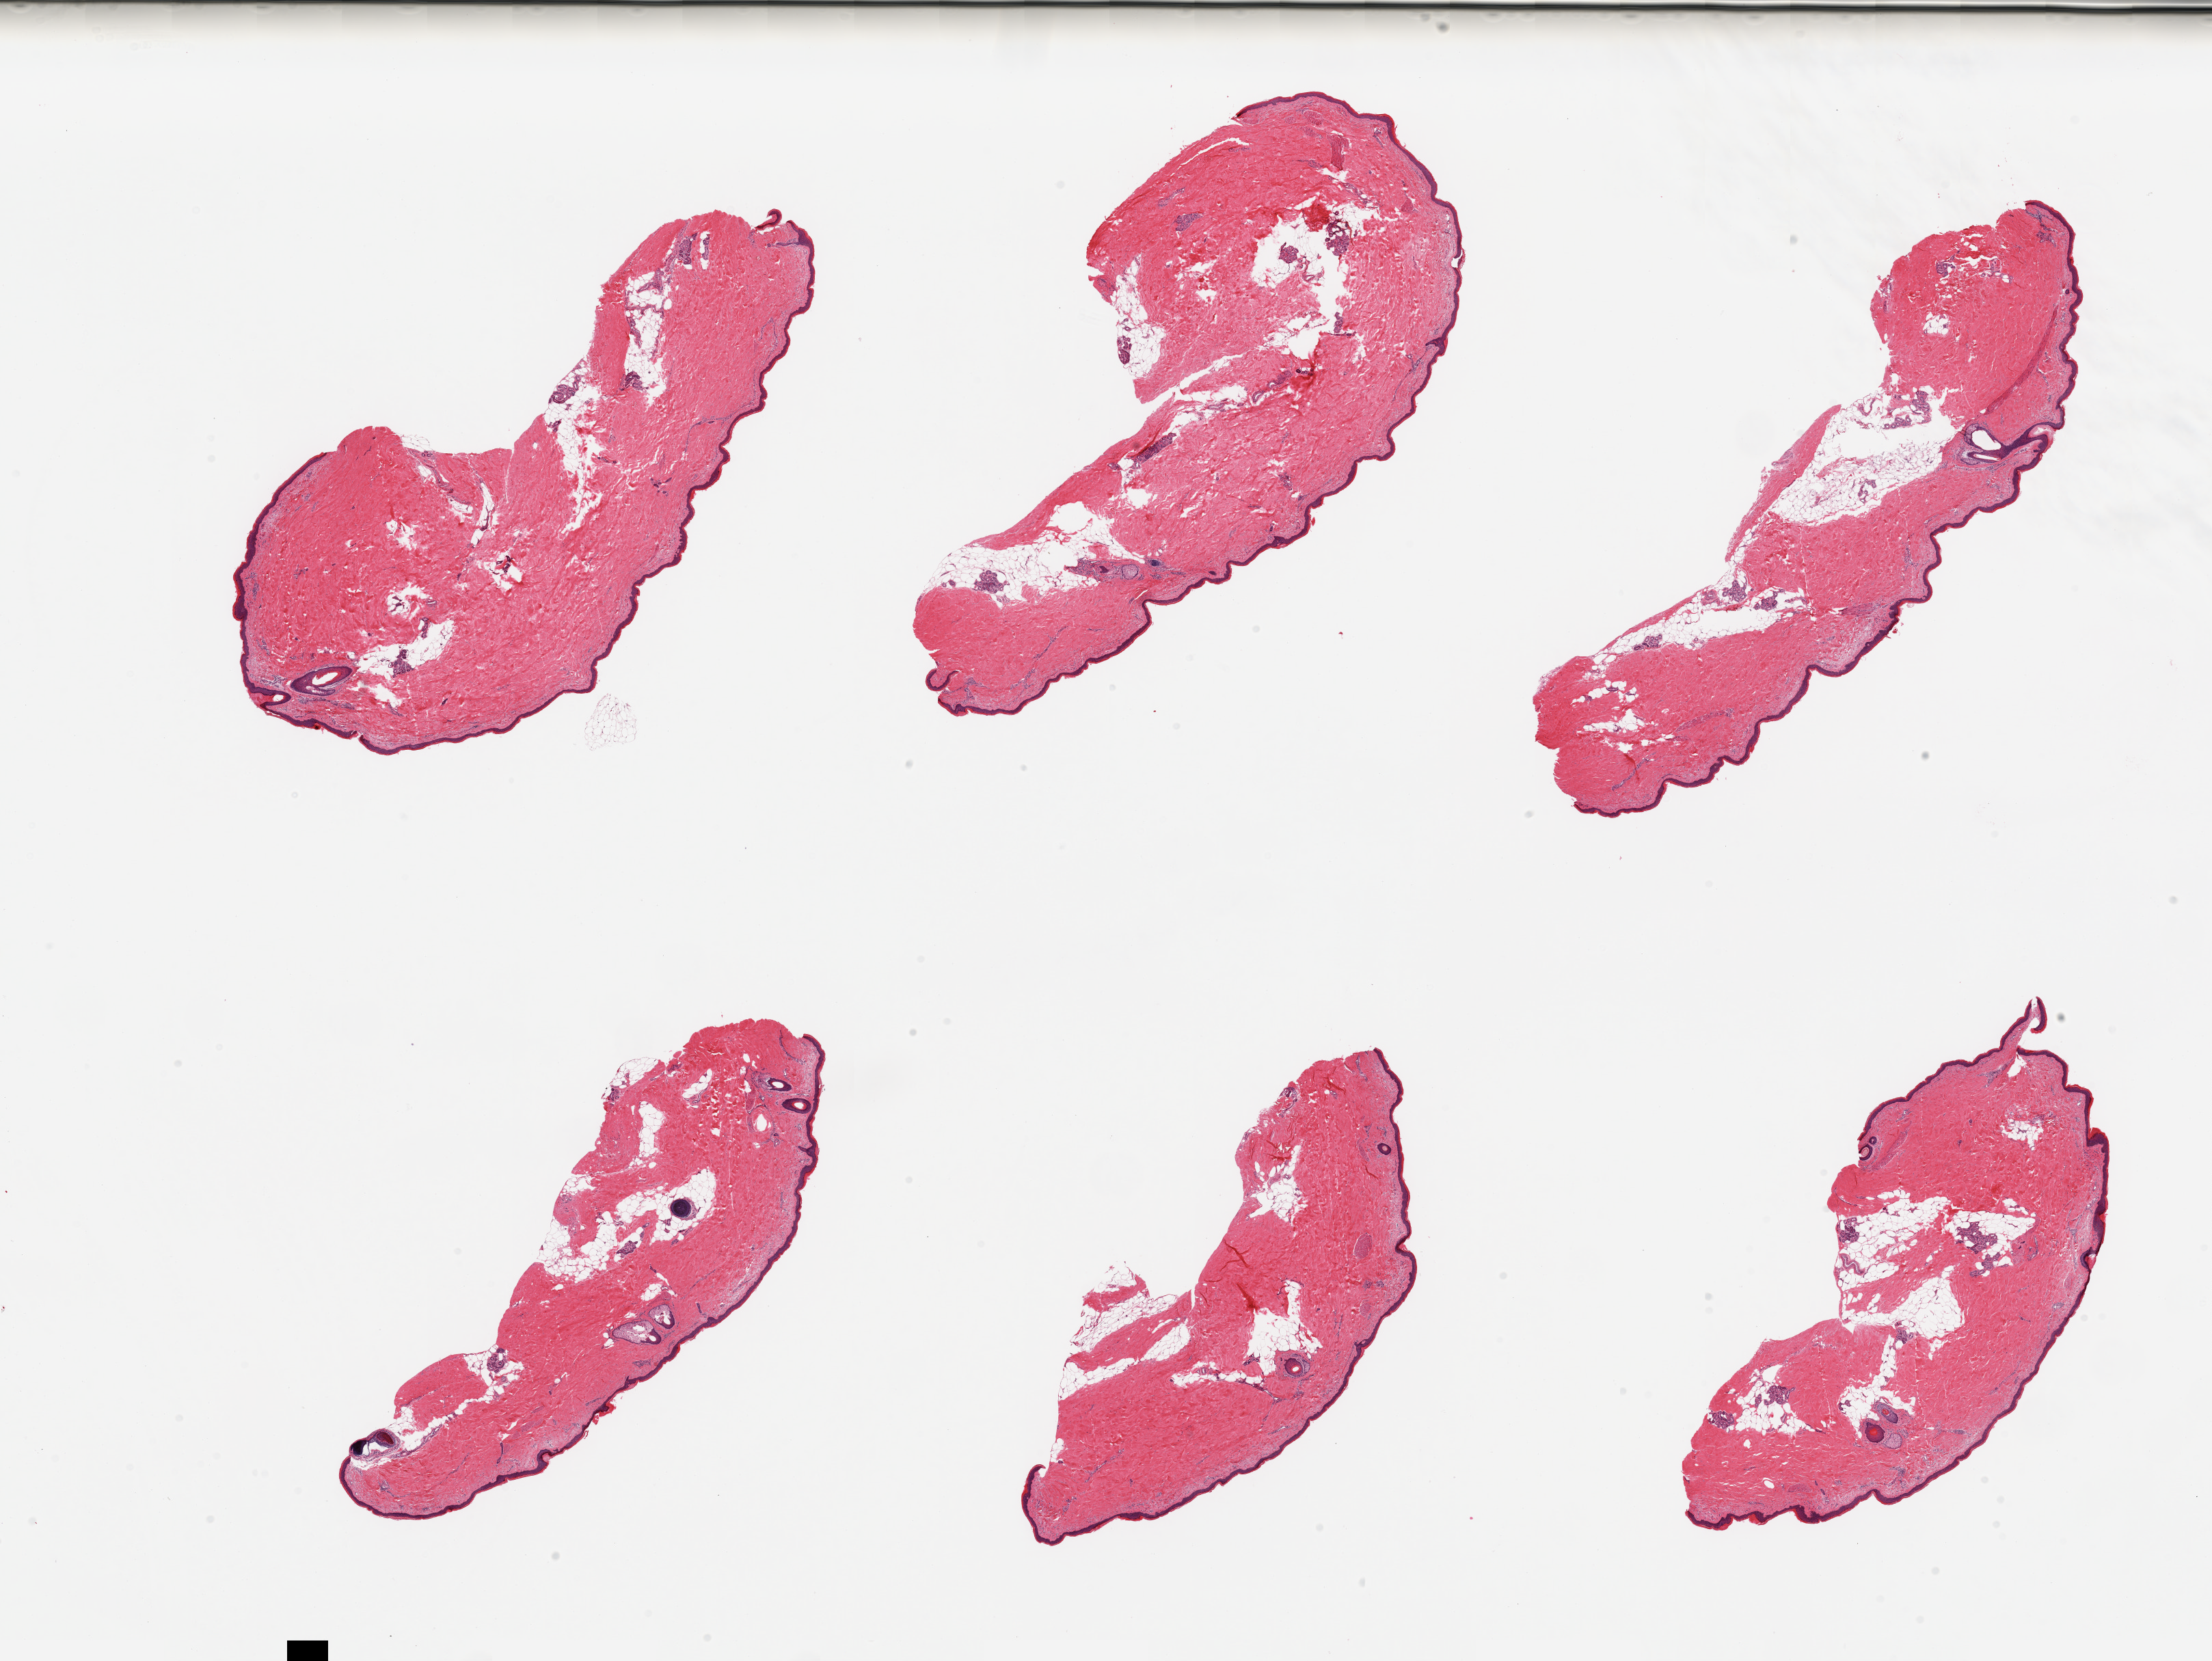
Whole-slide image, H&E stain — a low-resolution overview of the entire scanned area, about 25.6 x 19.2 mm (acquisition: 20x scan); PAXgene-fixed paraffin-embedded (PFPE) section; section of skin of lower leg (target tissue); tissue donor sample. Donor: male.
- reviewer comment on this tissue sample: 6 pieces; includes from 5-15% internal fat, epidermis measures 35 microns